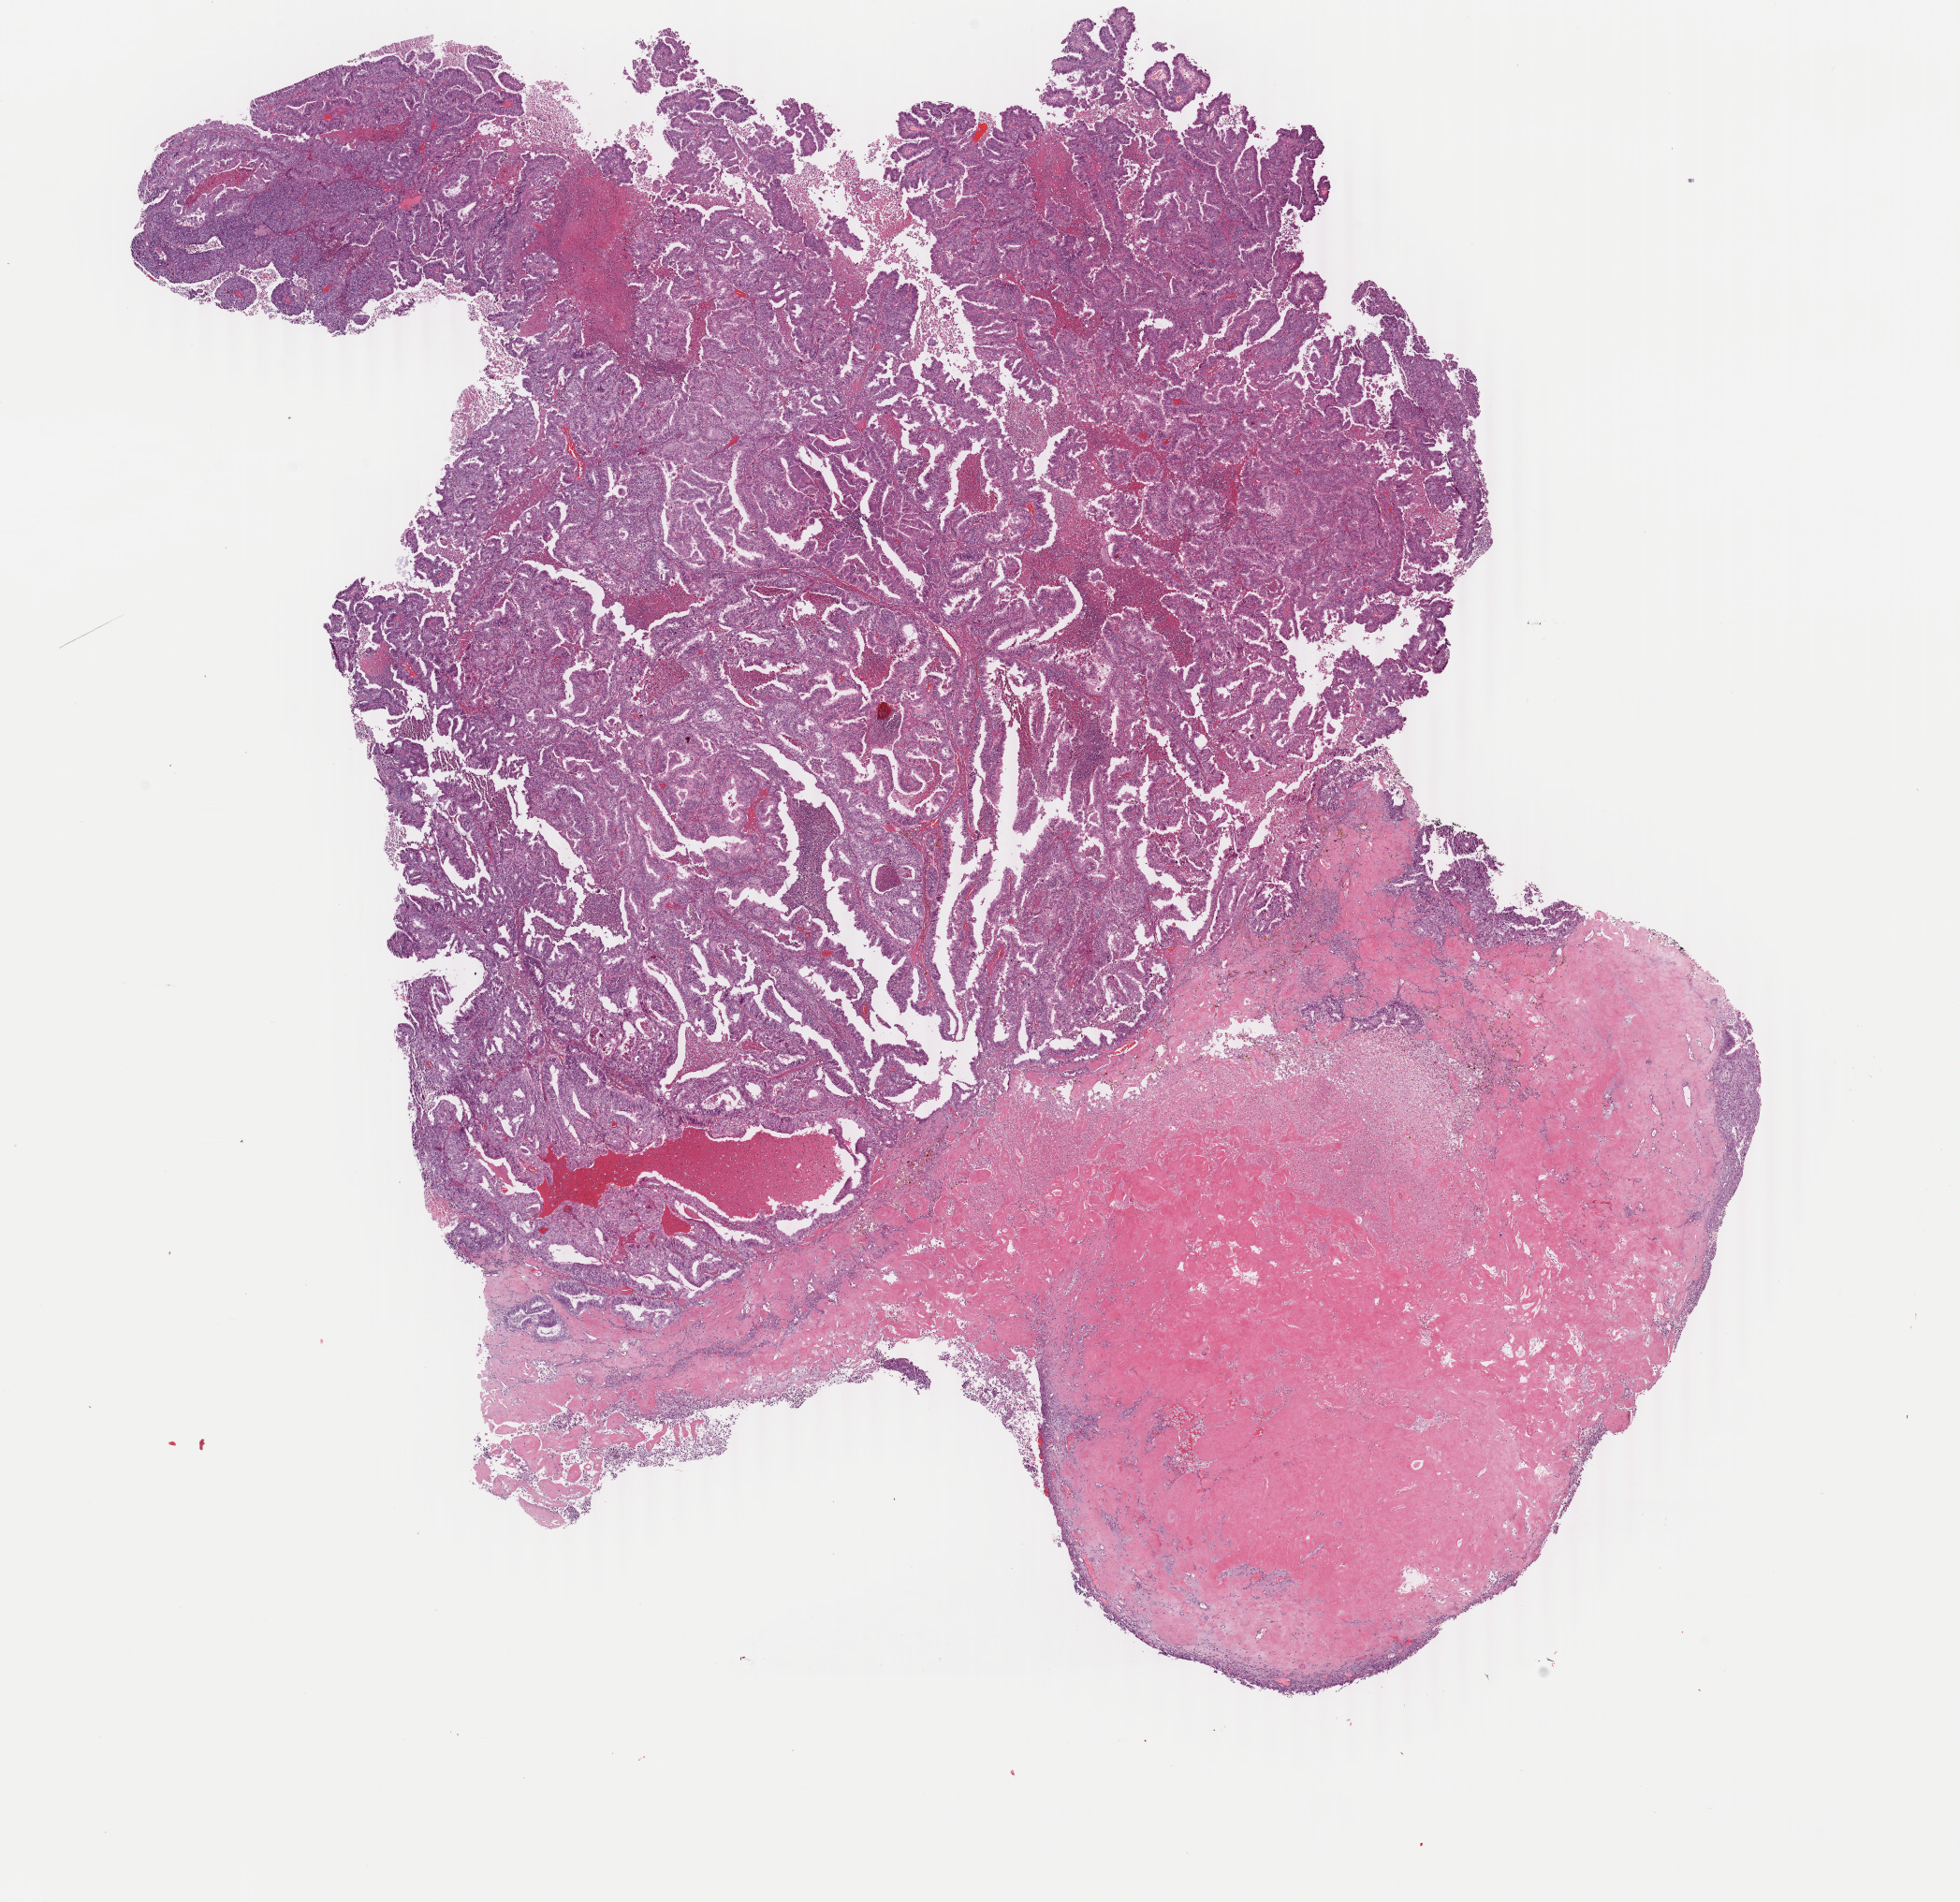
H&E whole-slide image — whole scanned area (about 16.7 x 16.2 mm, acquisition: 40x scan) shown as a low-resolution overview, frozen section, primary tumour sample from the uterus. Female, age 74 years at initial diagnosis.
Diagnosis: Endometrioid adenocarcinoma, NOS (endometrium).